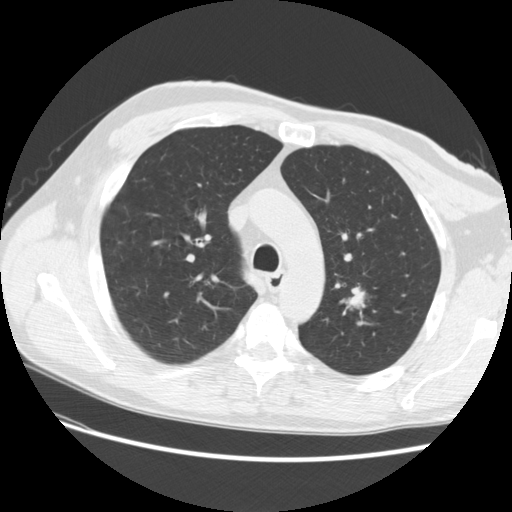
Low-dose screening chest CT, one axial slice; slice 186 of 256 in the series (ordered by position); reconstruction kernel STANDARD; 120 kVp; lung window (W 1500 / L -600 HU); 2.5 mm slice thickness; 512 × 512 image matrix.
Outlined on this slice (outlined manually by an expert reader):
- lesion 1 (tumor, upper lobe of left lung): bounding box (x1, y1, x2, y2) in pixels: (348, 290, 365, 306)